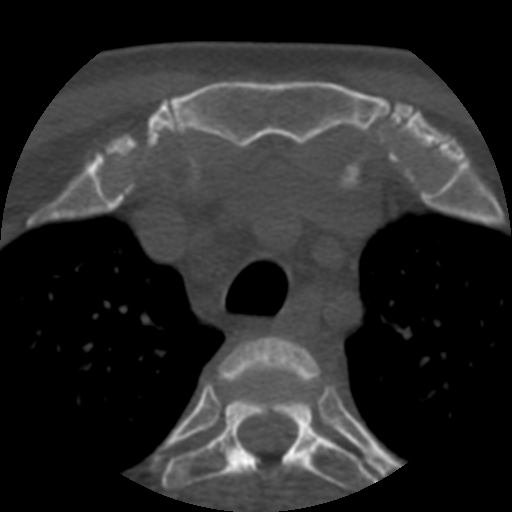
CT including the spine, one axial slice; position 419 of 508 along the scan axis; reconstruction kernel STANDARD; 120 kVp; bone window (W 1800 / L 400 HU); 1.25 mm slice thickness; 512 × 512 image matrix, field of view 160 × 160 mm. Patient age 57 years. From the clinical record (not read from this slice): primary cancer: prostate.
Outlined on this slice (semi-automatic segmentation, software-assisted and operator-edited):
- T2 vertebra: box from (x=219, y=335) to (x=320, y=390) px
- T3 vertebra: (x=162, y=385)–(x=377, y=489)